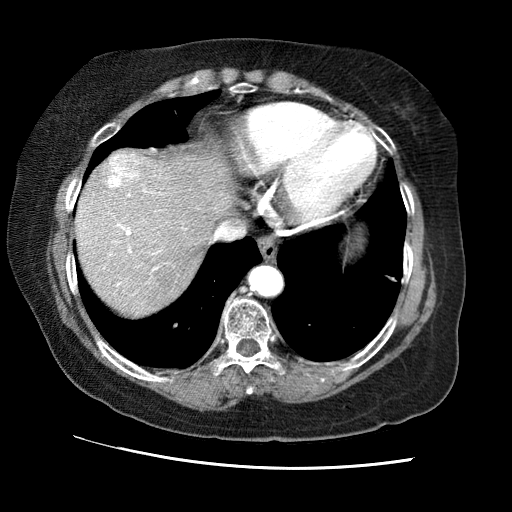
Contrast-enhanced abdominal CT (liver protocol), one axial slice; soft-tissue window (W 400 / L 40 HU); 2.5 mm slice thickness; 512 × 512 image matrix, field of view 340 × 340 mm. From the clinical record (not read from this slice): diagnosis: hepatocellular carcinoma (patient treated with transarterial chemoembolisation; whether this scan precedes or follows treatment is not stated here); TNM stage (as recorded): Stage-II; Child-Pugh class: A.
Outlined on this slice (semi-automatic segmentation, software-assisted and operator-edited):
- abdominal aorta: bounding box [x1, y1, x2, y2] px = [251, 267, 282, 295]
- liver parenchyma outside the tumour (the mass and vessels are separate outlines, so this box may not span the whole liver): [76, 150, 234, 316]
- mass: [107, 150, 141, 188]
- liver vessels: [81, 173, 186, 286]